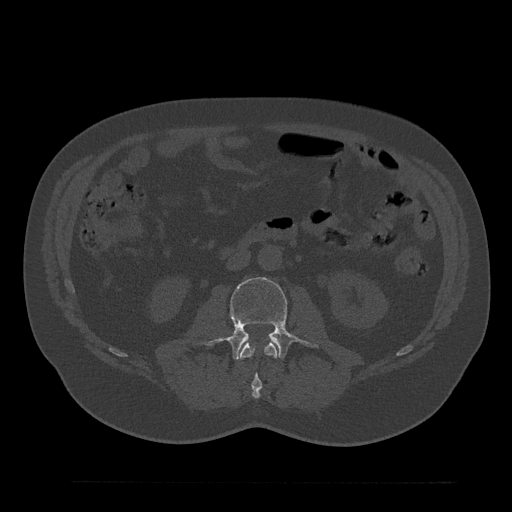
CT including the spine, one axial slice; position 56 of 797 along the scan axis; reconstruction kernel Br40s/3; bone window (W 1800 / L 400 HU); 0.5 mm slice thickness; 512 × 512 image matrix. Male patient, age 61 years. Case-level facts recorded for this patient, not image findings: primary cancer: prostate.
Annotated regions visible in this slice (semi-automatically segmented with operator editing):
- L2 vertebra: bounding box (x1, y1, x2, y2) in pixels: (239, 342, 278, 399)
- L3 vertebra: (212, 277, 314, 359)